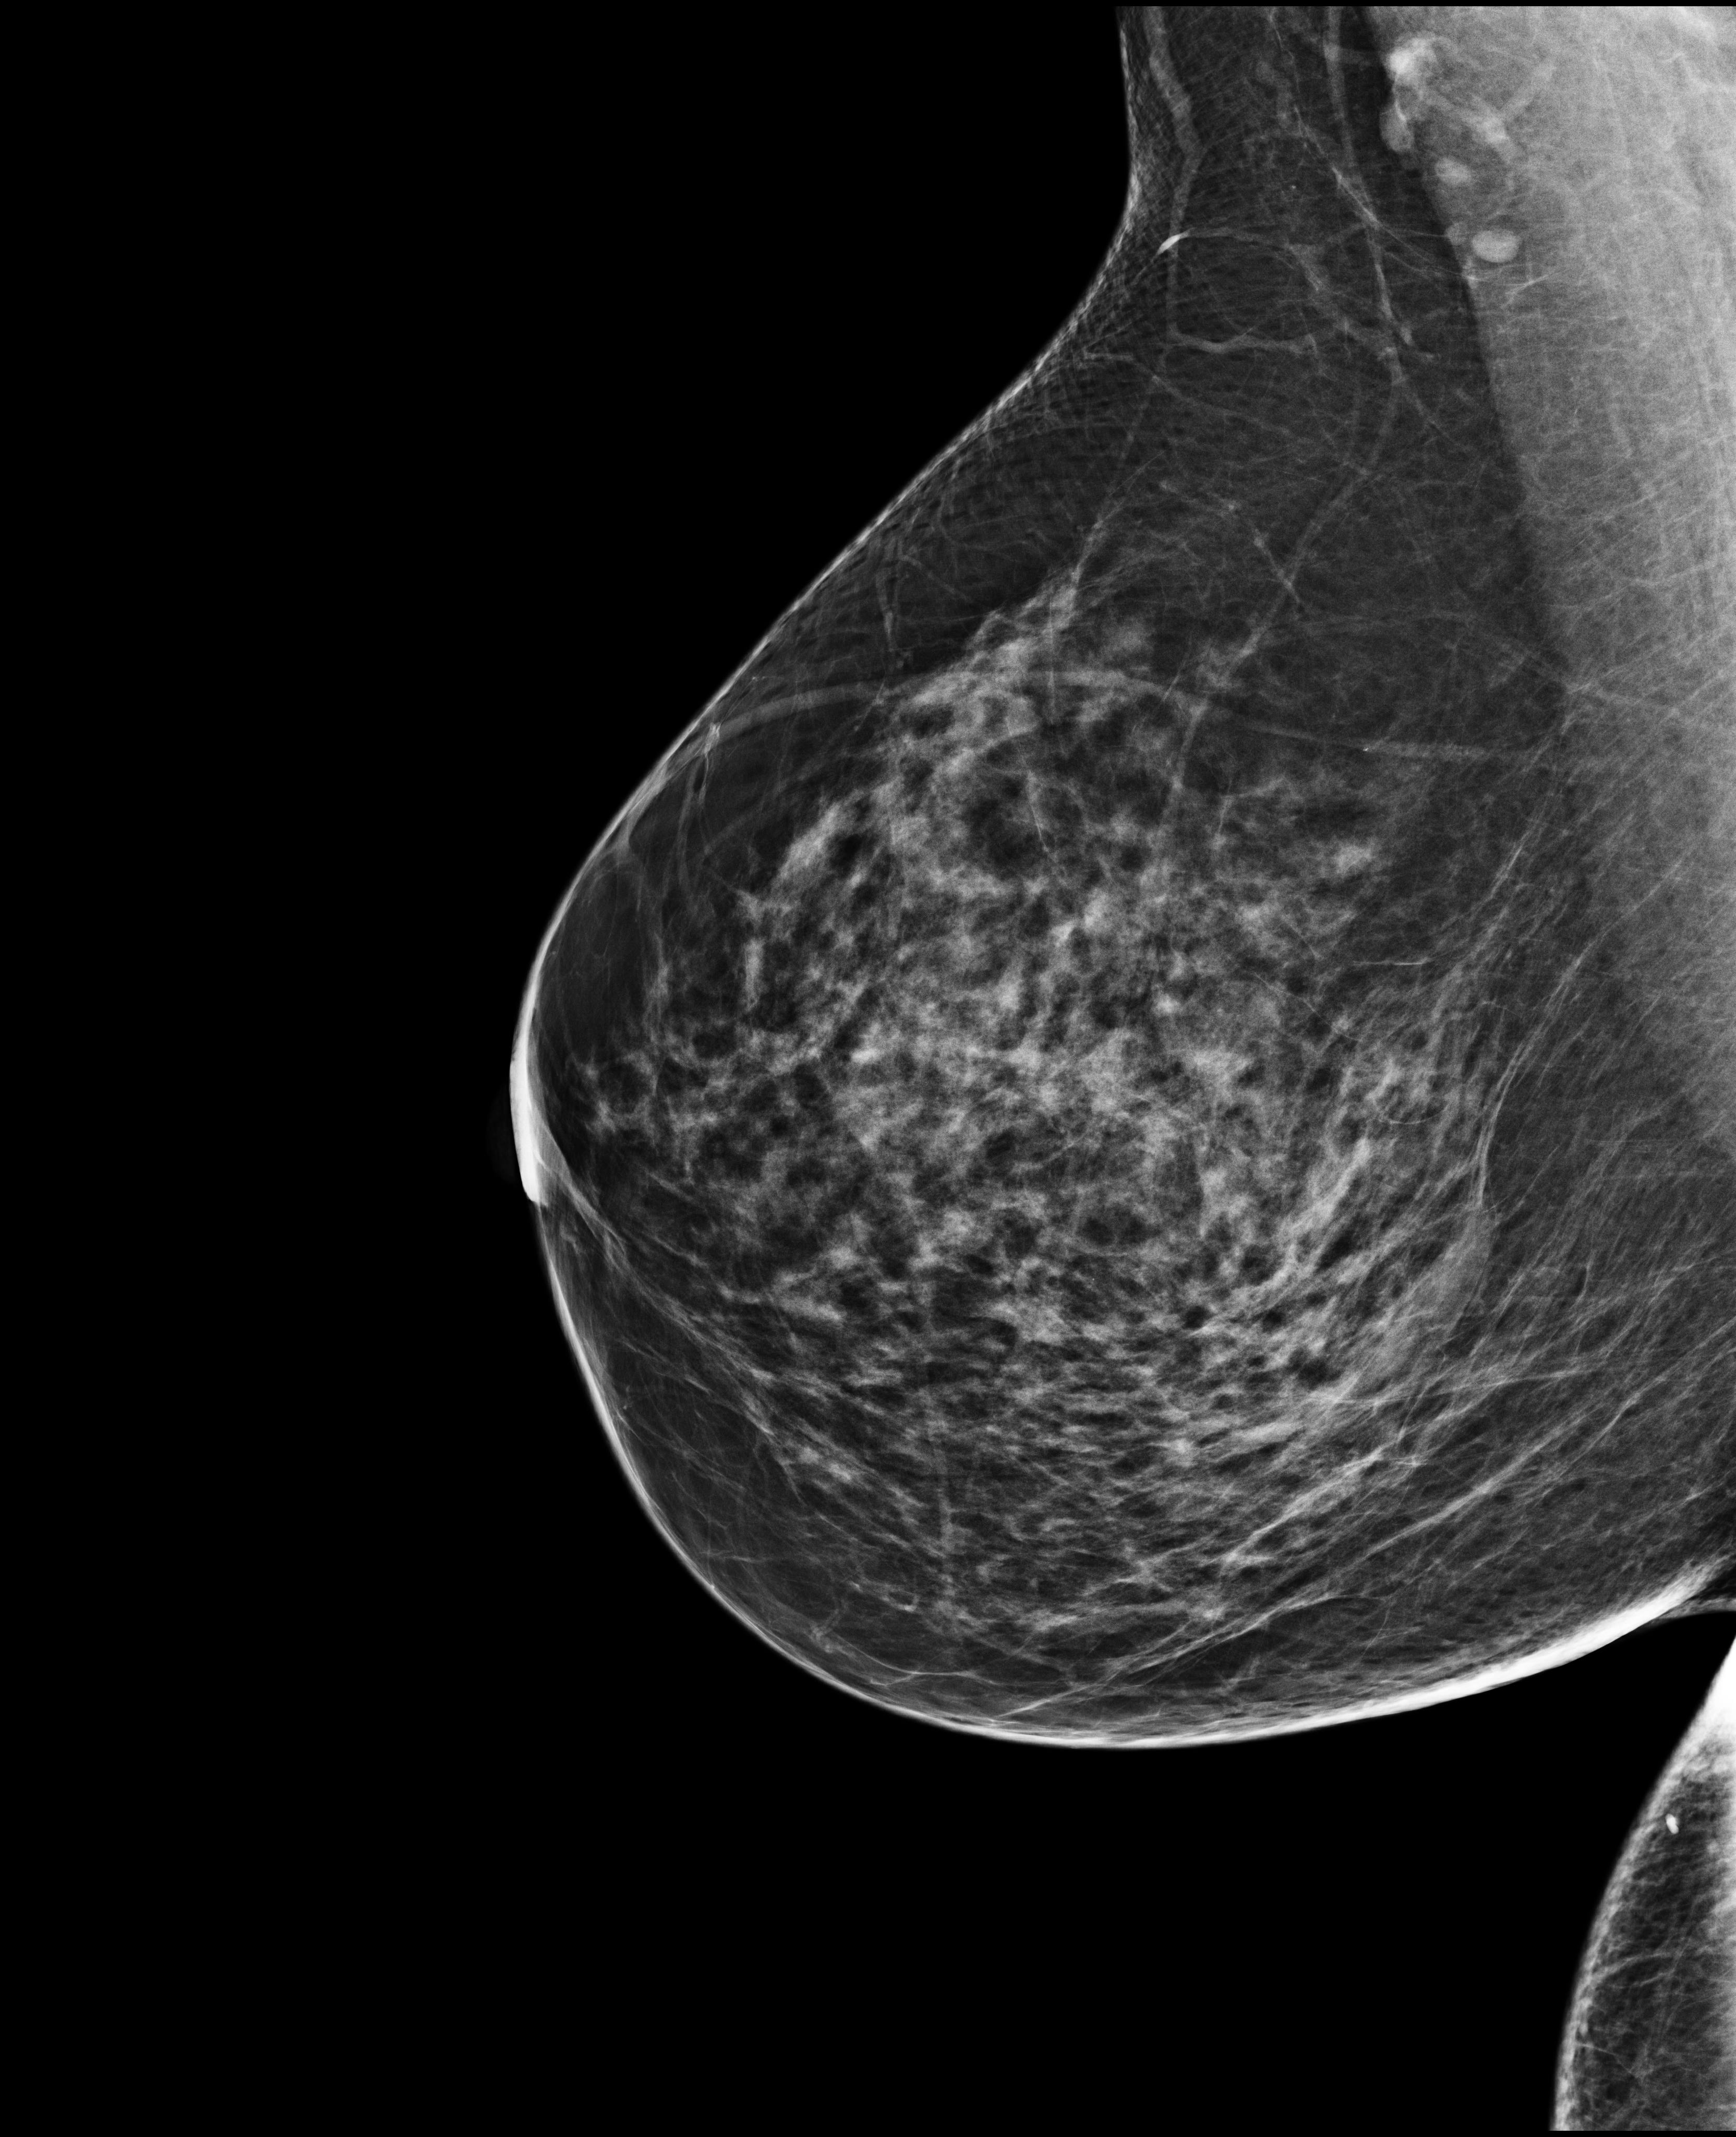
Annual screening mammography examination. Patient: female, 51 years.
Image type: full-field digital mammogram. Breast: right. Projection: MLO view.